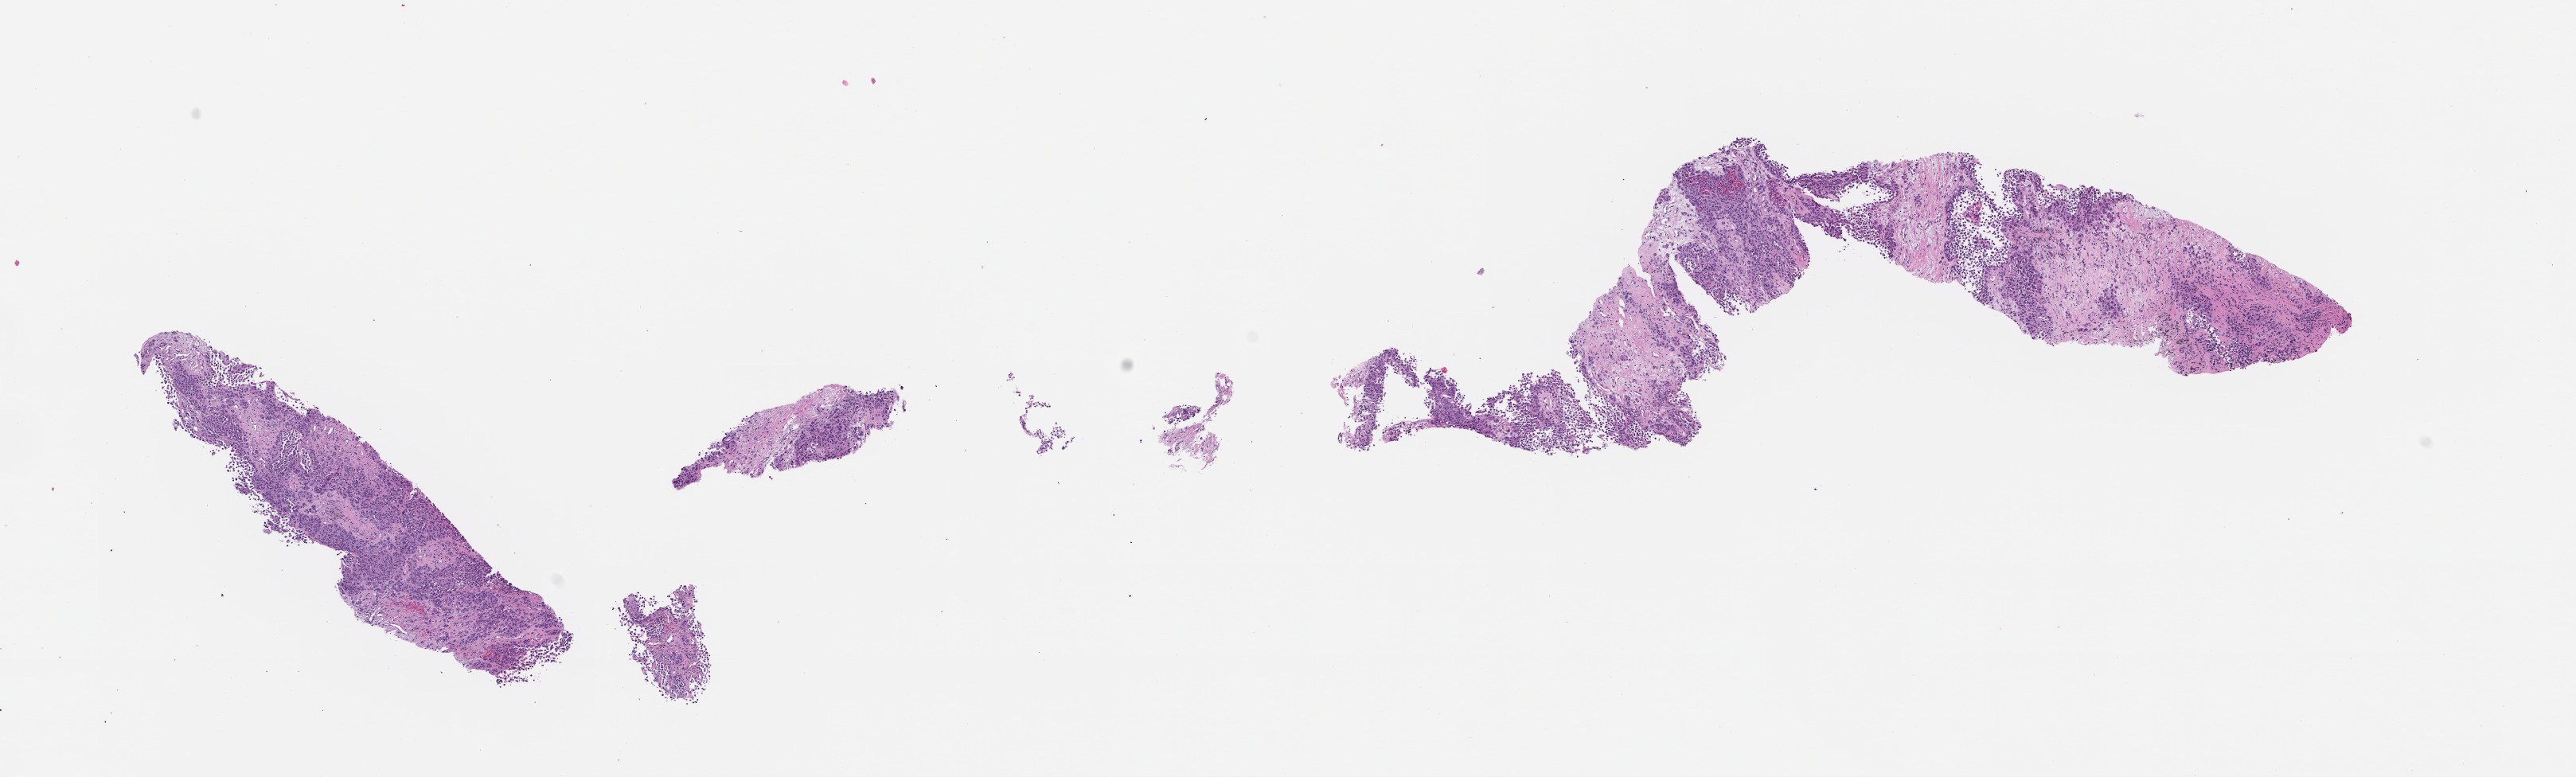
Hematoxylin and eosin (H&E) whole-slide image, a low-resolution overview of the entire scanned area, about 13.1 x 3.9 mm. Formalin-fixed paraffin-embedded section. Patient: male.
This section: metastasis (sampled organ not recorded). Primary diagnosis of the patient: Melanoma.